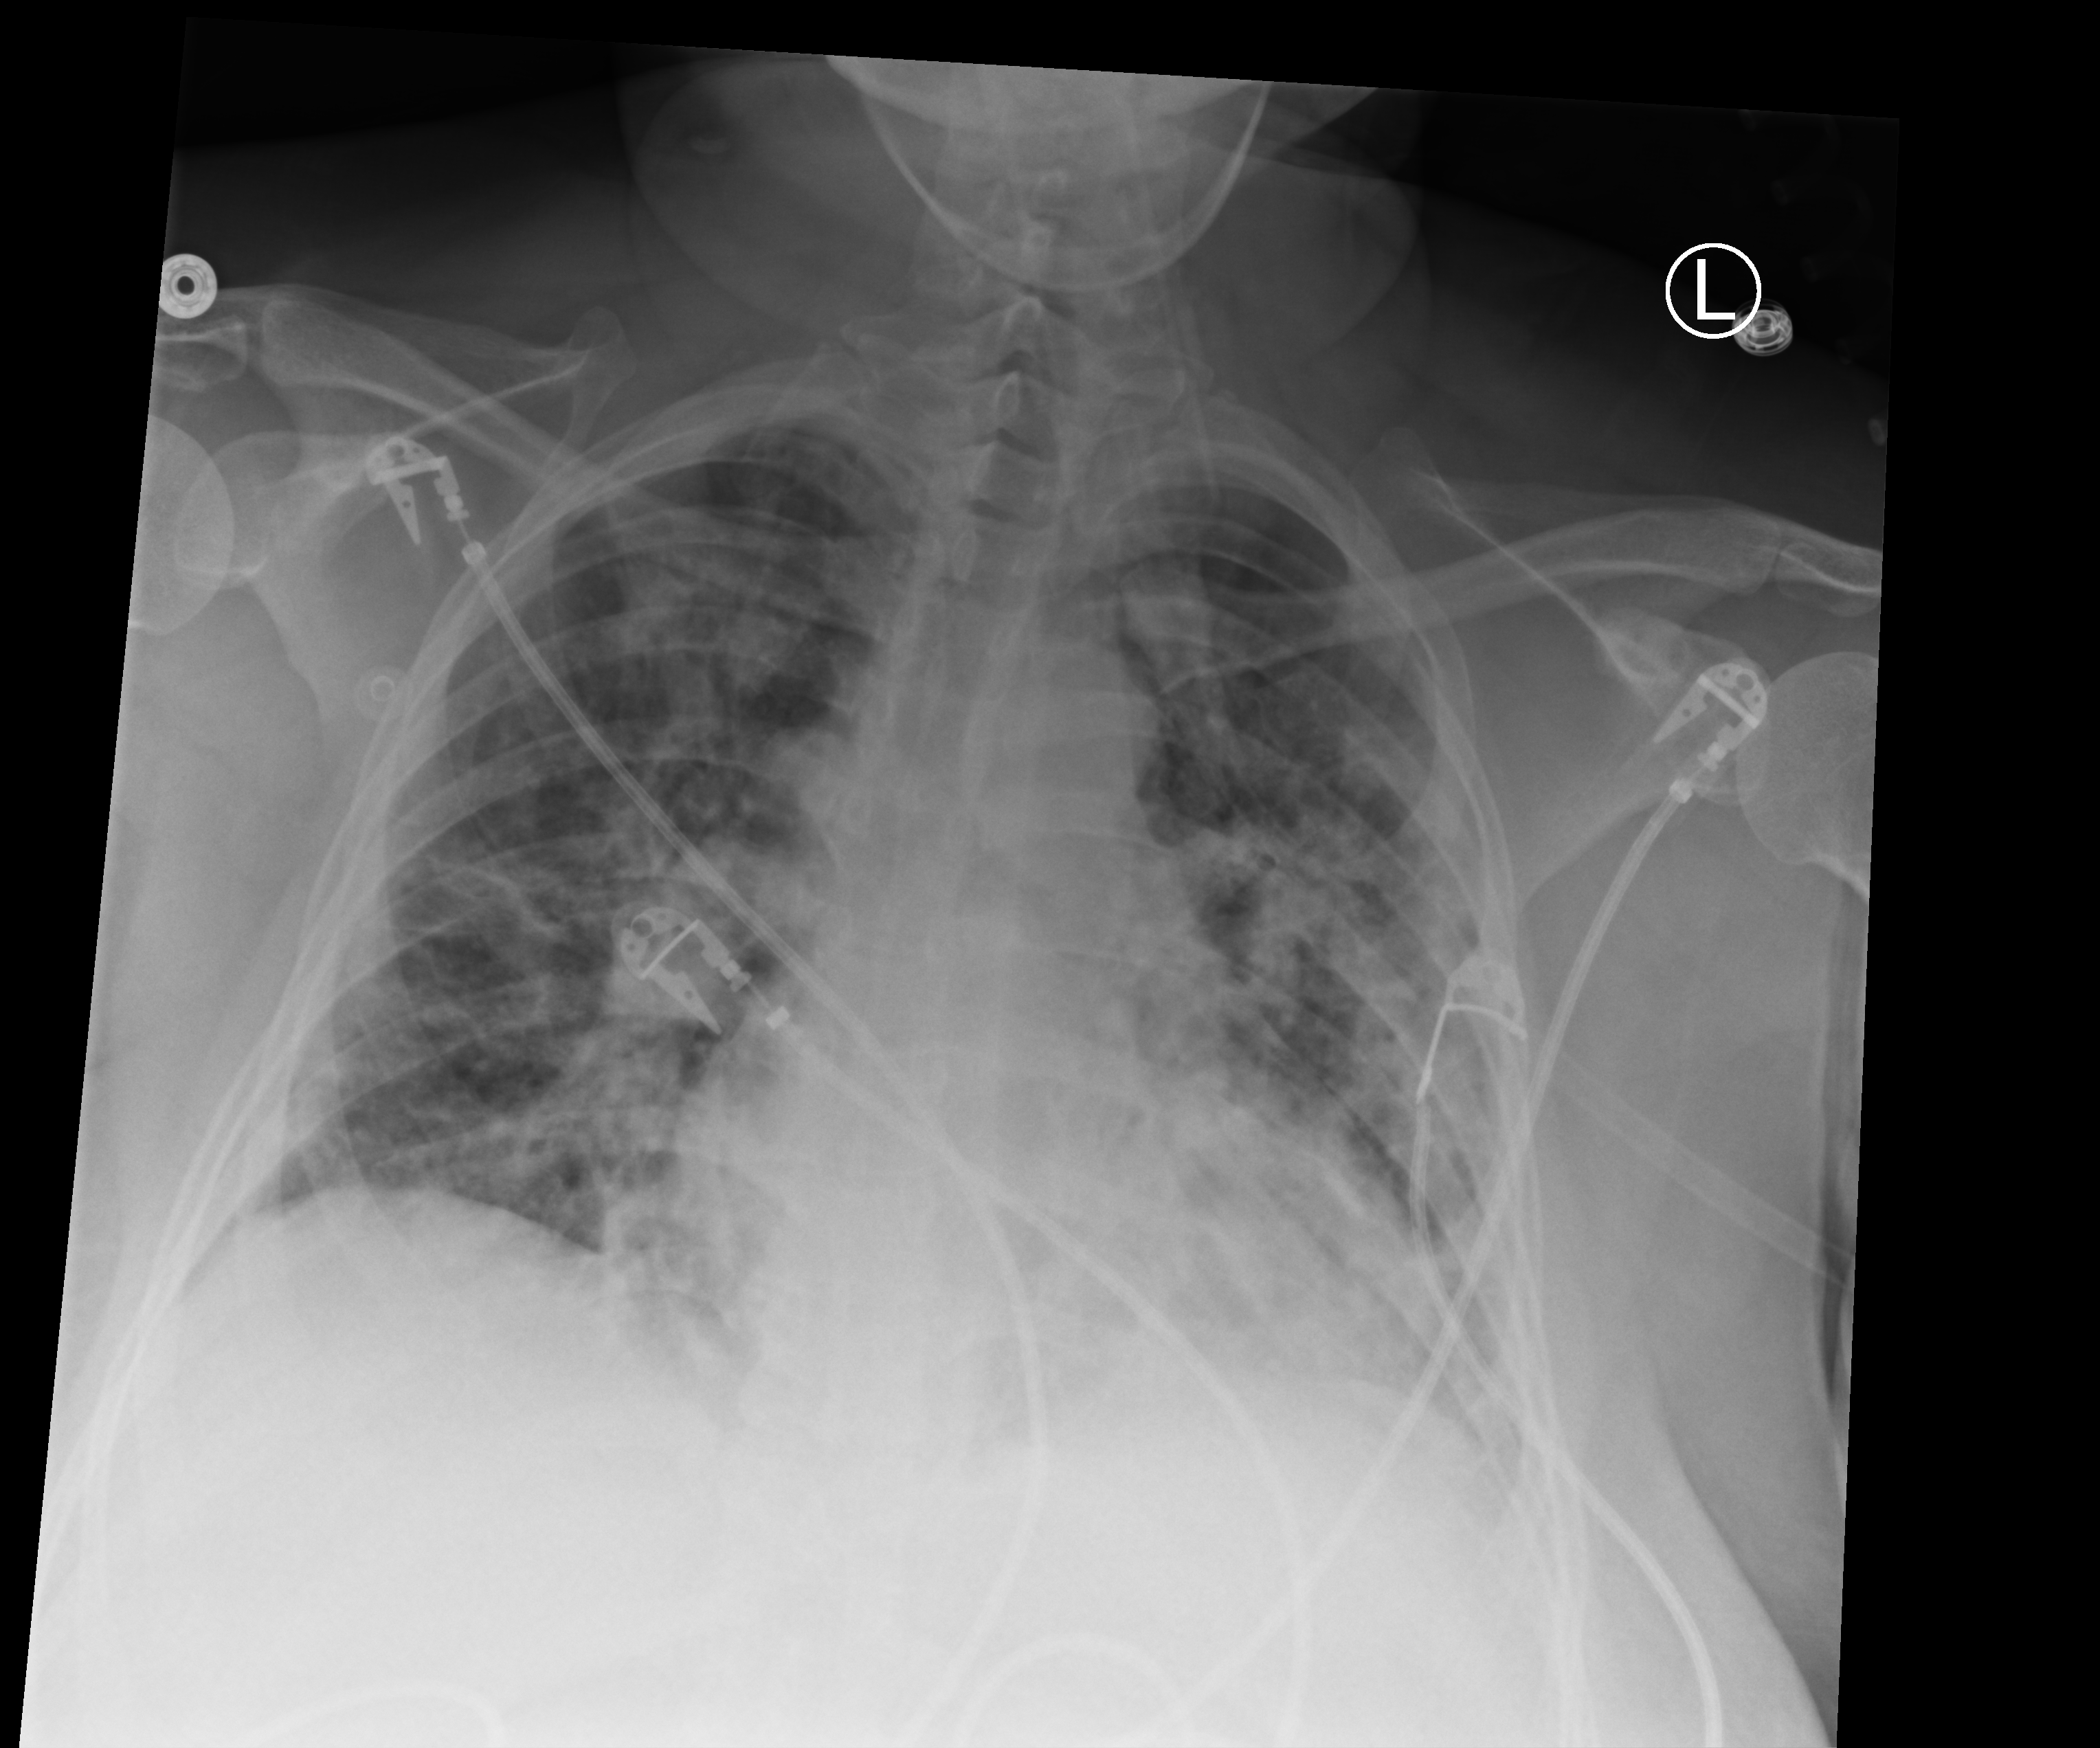
Chest X-ray (portable). Female patient hospitalised with COVID-19, age 18–59 years.
From the hospital-stay record, not from the radiograph (when in the stay this image was taken is not recorded):
- mechanically ventilated during this hospital stay: yes
- admitted to intensive care during this hospital stay: yes
- hypertension (admission record): no